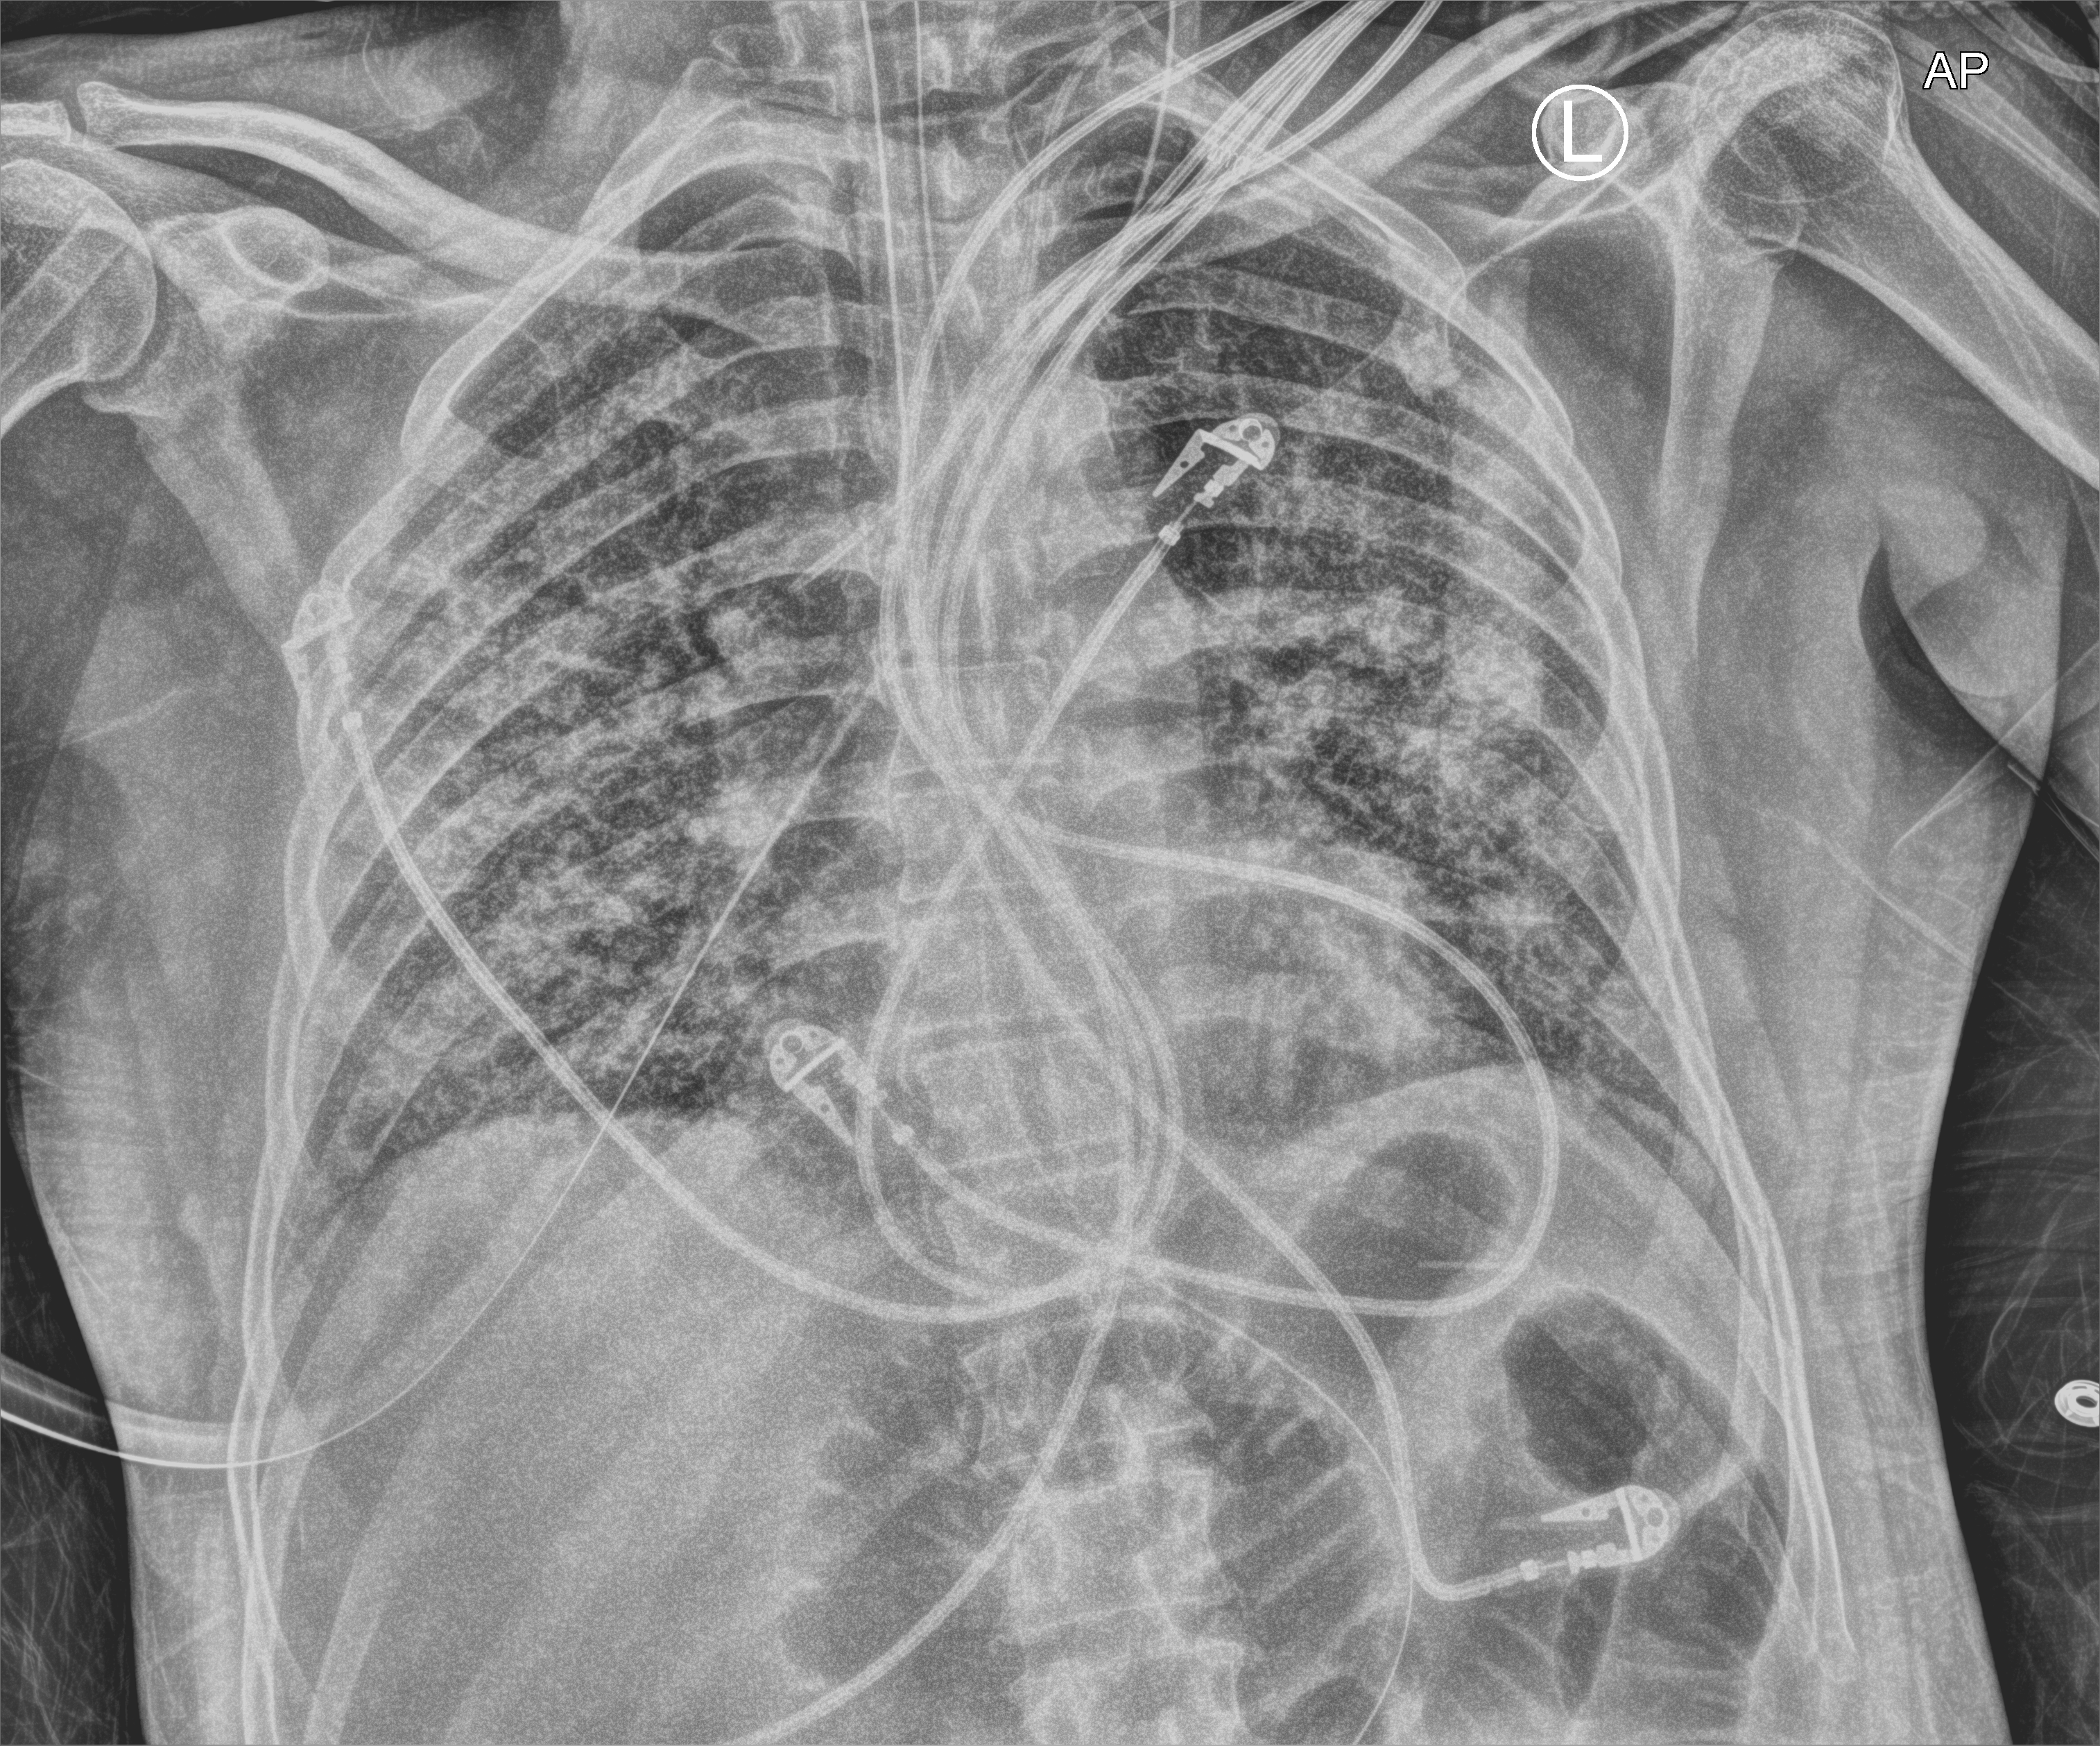
Portable chest radiograph, anteroposterior (AP) projection. Male patient hospitalised with COVID-19, age 60–74 years.
Admission-level facts for this patient (not findings on this image; timing relative to this image not recorded): admitted to intensive care during this hospital stay: yes; diabetes (admission record): no; hypertension (admission record): no.